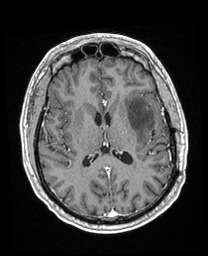
Brain MRI from a brain-tumour surgery series, one axial slice; position 101 of 208 along the scan axis; T1-weighted post-contrast; 208 × 256 image matrix, field of view 211 × 260 mm. From the clinical record (not read from this slice): histopathology: Astrocytoma; WHO grade: 3; IDH mutation: yes.
Annotated regions visible in this slice (expert manual segmentation):
- previous resection cavity: bounding box [x1, y1, x2, y2] px = [152, 131, 154, 136]